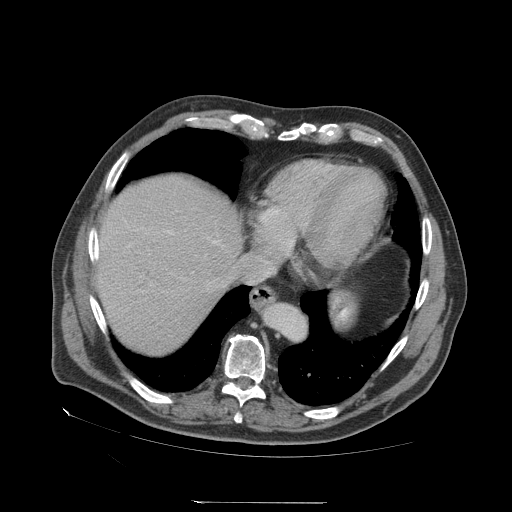
Contrast-enhanced abdominal CT (liver protocol), one axial slice; slice 62 of 83 in the series (ordered by position); reconstruction kernel STANDARD; 140 kVp; soft-tissue window (W 400 / L 40 HU); 2.5 mm slice thickness; 512 × 512 image matrix. From the clinical record (not read from this slice): diagnosis: hepatocellular carcinoma (patient treated with transarterial chemoembolisation; whether this scan precedes or follows treatment is not stated here); TNM stage (as recorded): Stage-I; Child-Pugh class: A.
Structures marked on this image (semi-automatic segmentation, software-assisted and operator-edited):
- abdominal aorta: box from (x=266, y=305) to (x=305, y=339) px
- liver parenchyma outside the tumour (the mass and vessels are separate outlines, so this box may not span the whole liver): (x=96, y=174)–(x=242, y=354)
- liver vessels: (x=168, y=231)–(x=217, y=243)